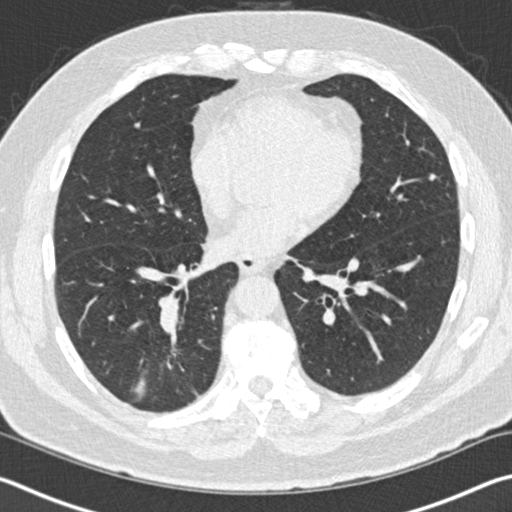
Low-dose screening chest CT, one axial slice. Position 48 of 141 along the scan axis. Reconstruction kernel B30f. 120 kVp. Lung window (W 1500 / L -600 HU). 2 mm slice thickness. 512 × 512 image matrix, field of view 344 × 344 mm.
Structures marked on this image (expert manual segmentation):
- lesion 1 (tumor, lower lobe of right lung): box from (x=171, y=334) to (x=177, y=353) px